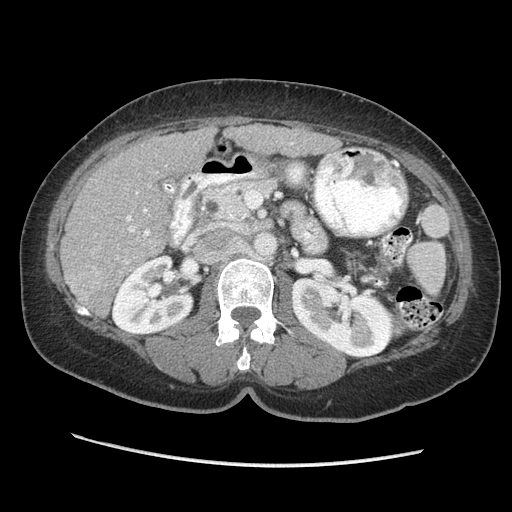
Contrast-enhanced abdominal CT (liver protocol), one axial slice; position 115 of 170 along the scan axis; reconstruction kernel STANDARD; soft-tissue window (W 400 / L 40 HU); 512 × 512 image matrix, field of view 360 × 360 mm. Case-level facts recorded for this patient, not image findings: diagnosis: hepatocellular carcinoma (patient treated with transarterial chemoembolisation; whether this scan precedes or follows treatment is not stated here); TNM stage (as recorded): Stage-II; Child-Pugh class: A; tumour differentiation: no biopsy; tumour nodularity: multinodular.
Annotated regions visible in this slice (semi-automatically segmented with operator editing):
- liver parenchyma outside the tumour (the mass and vessels are separate outlines, so this box may not span the whole liver): bounding box <60,124,340,316> (left, top, right, bottom; pixels)
- liver vessels: <97,142,293,274>